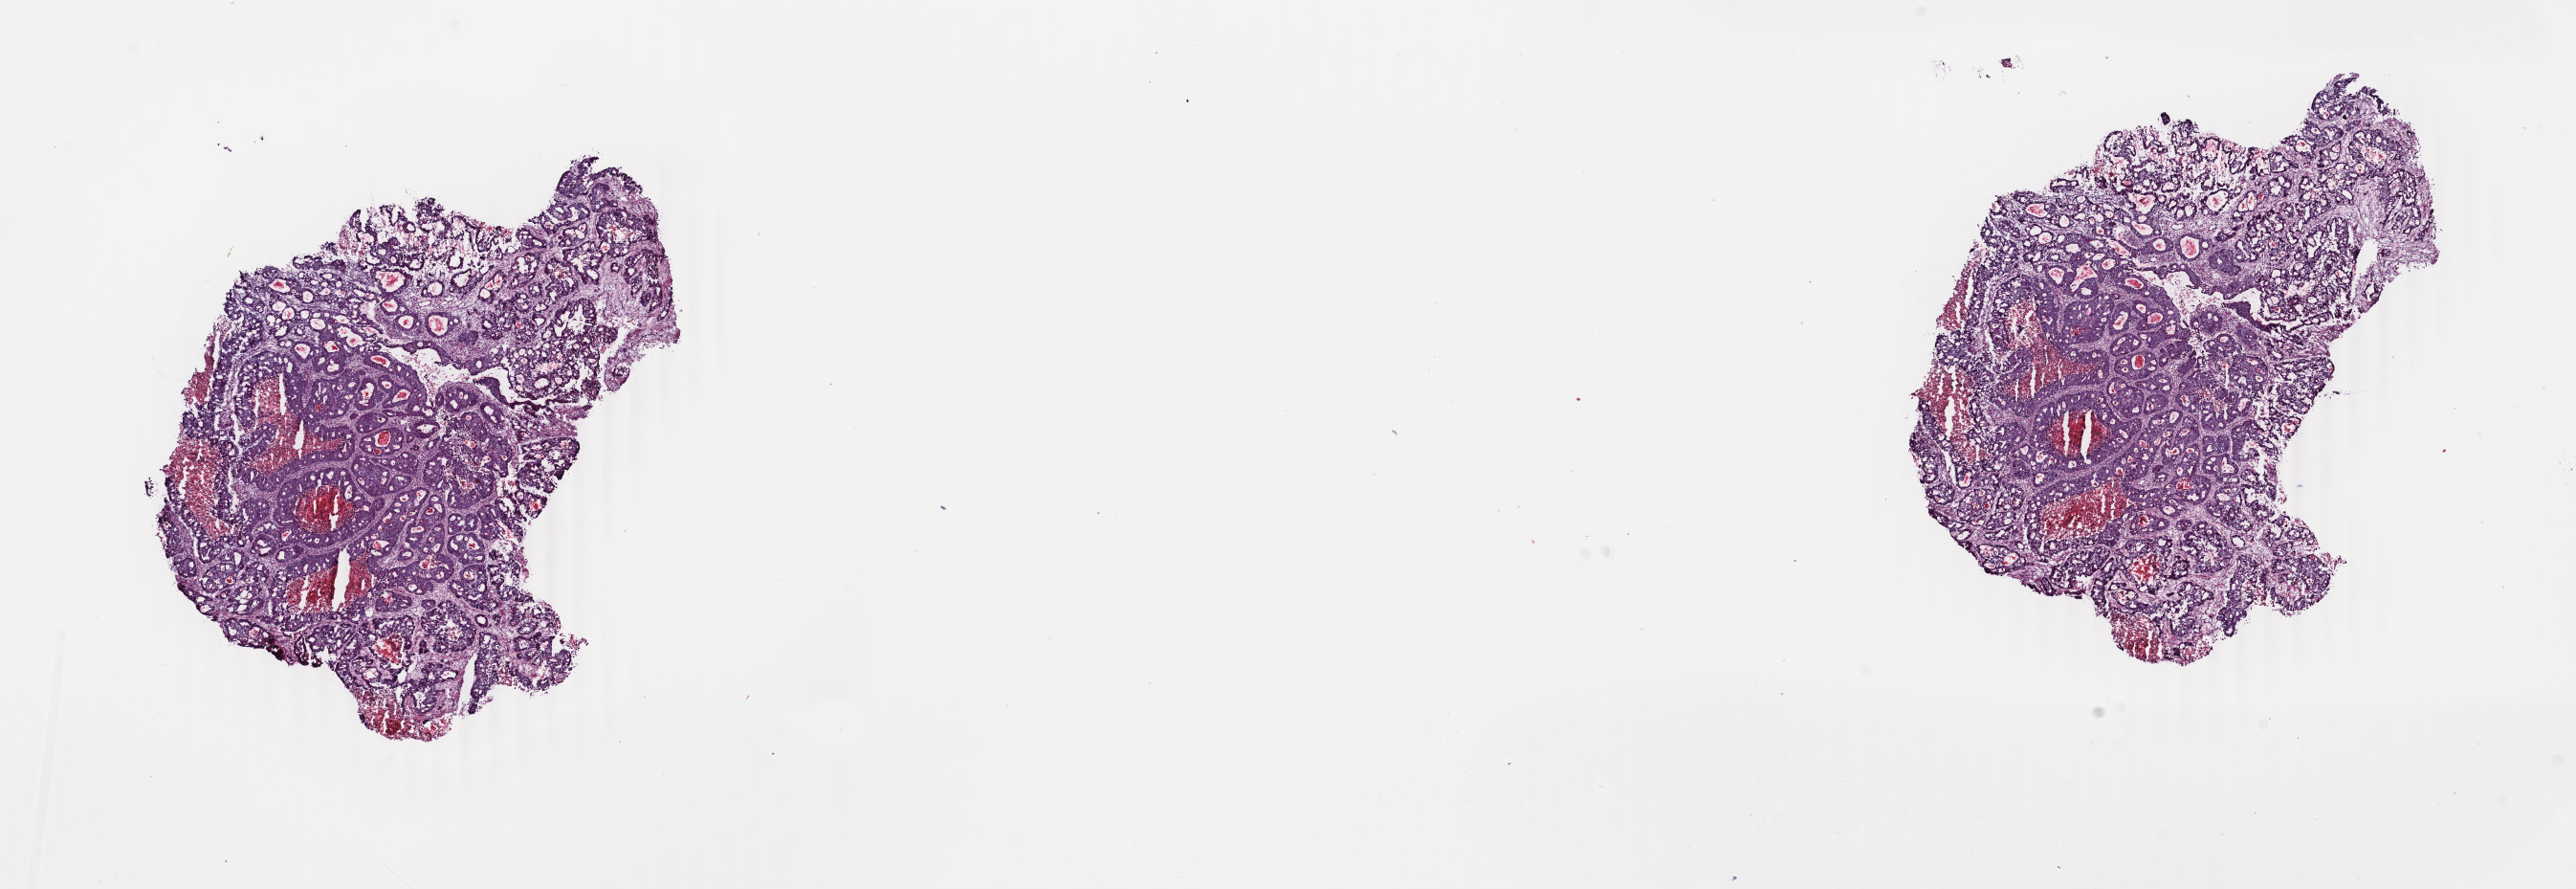
Whole-slide histology image, Hematoxylin and eosin (H&E) stained, low-resolution overview of the scanned area, about 21.4 x 7.4 mm (from a 40x scan), frozen section from the top of the tissue portion, metastatic tumour sample, sampled site not recorded. Female, age 53 years at initial diagnosis. Composition of this section per pathologist review: tumour cells 70%, tumour nuclei 70%, normal cells 5%, stromal cells 20%, necrosis 5%. Inflammatory infiltration, as recorded: lymphocyte infiltration 3%, monocyte infiltration 0%, neutrophil infiltration 0%.
This section: metastatic tumour tissue. Patient diagnosis: Adenocarcinoma, NOS (primary site: sigmoid colon).